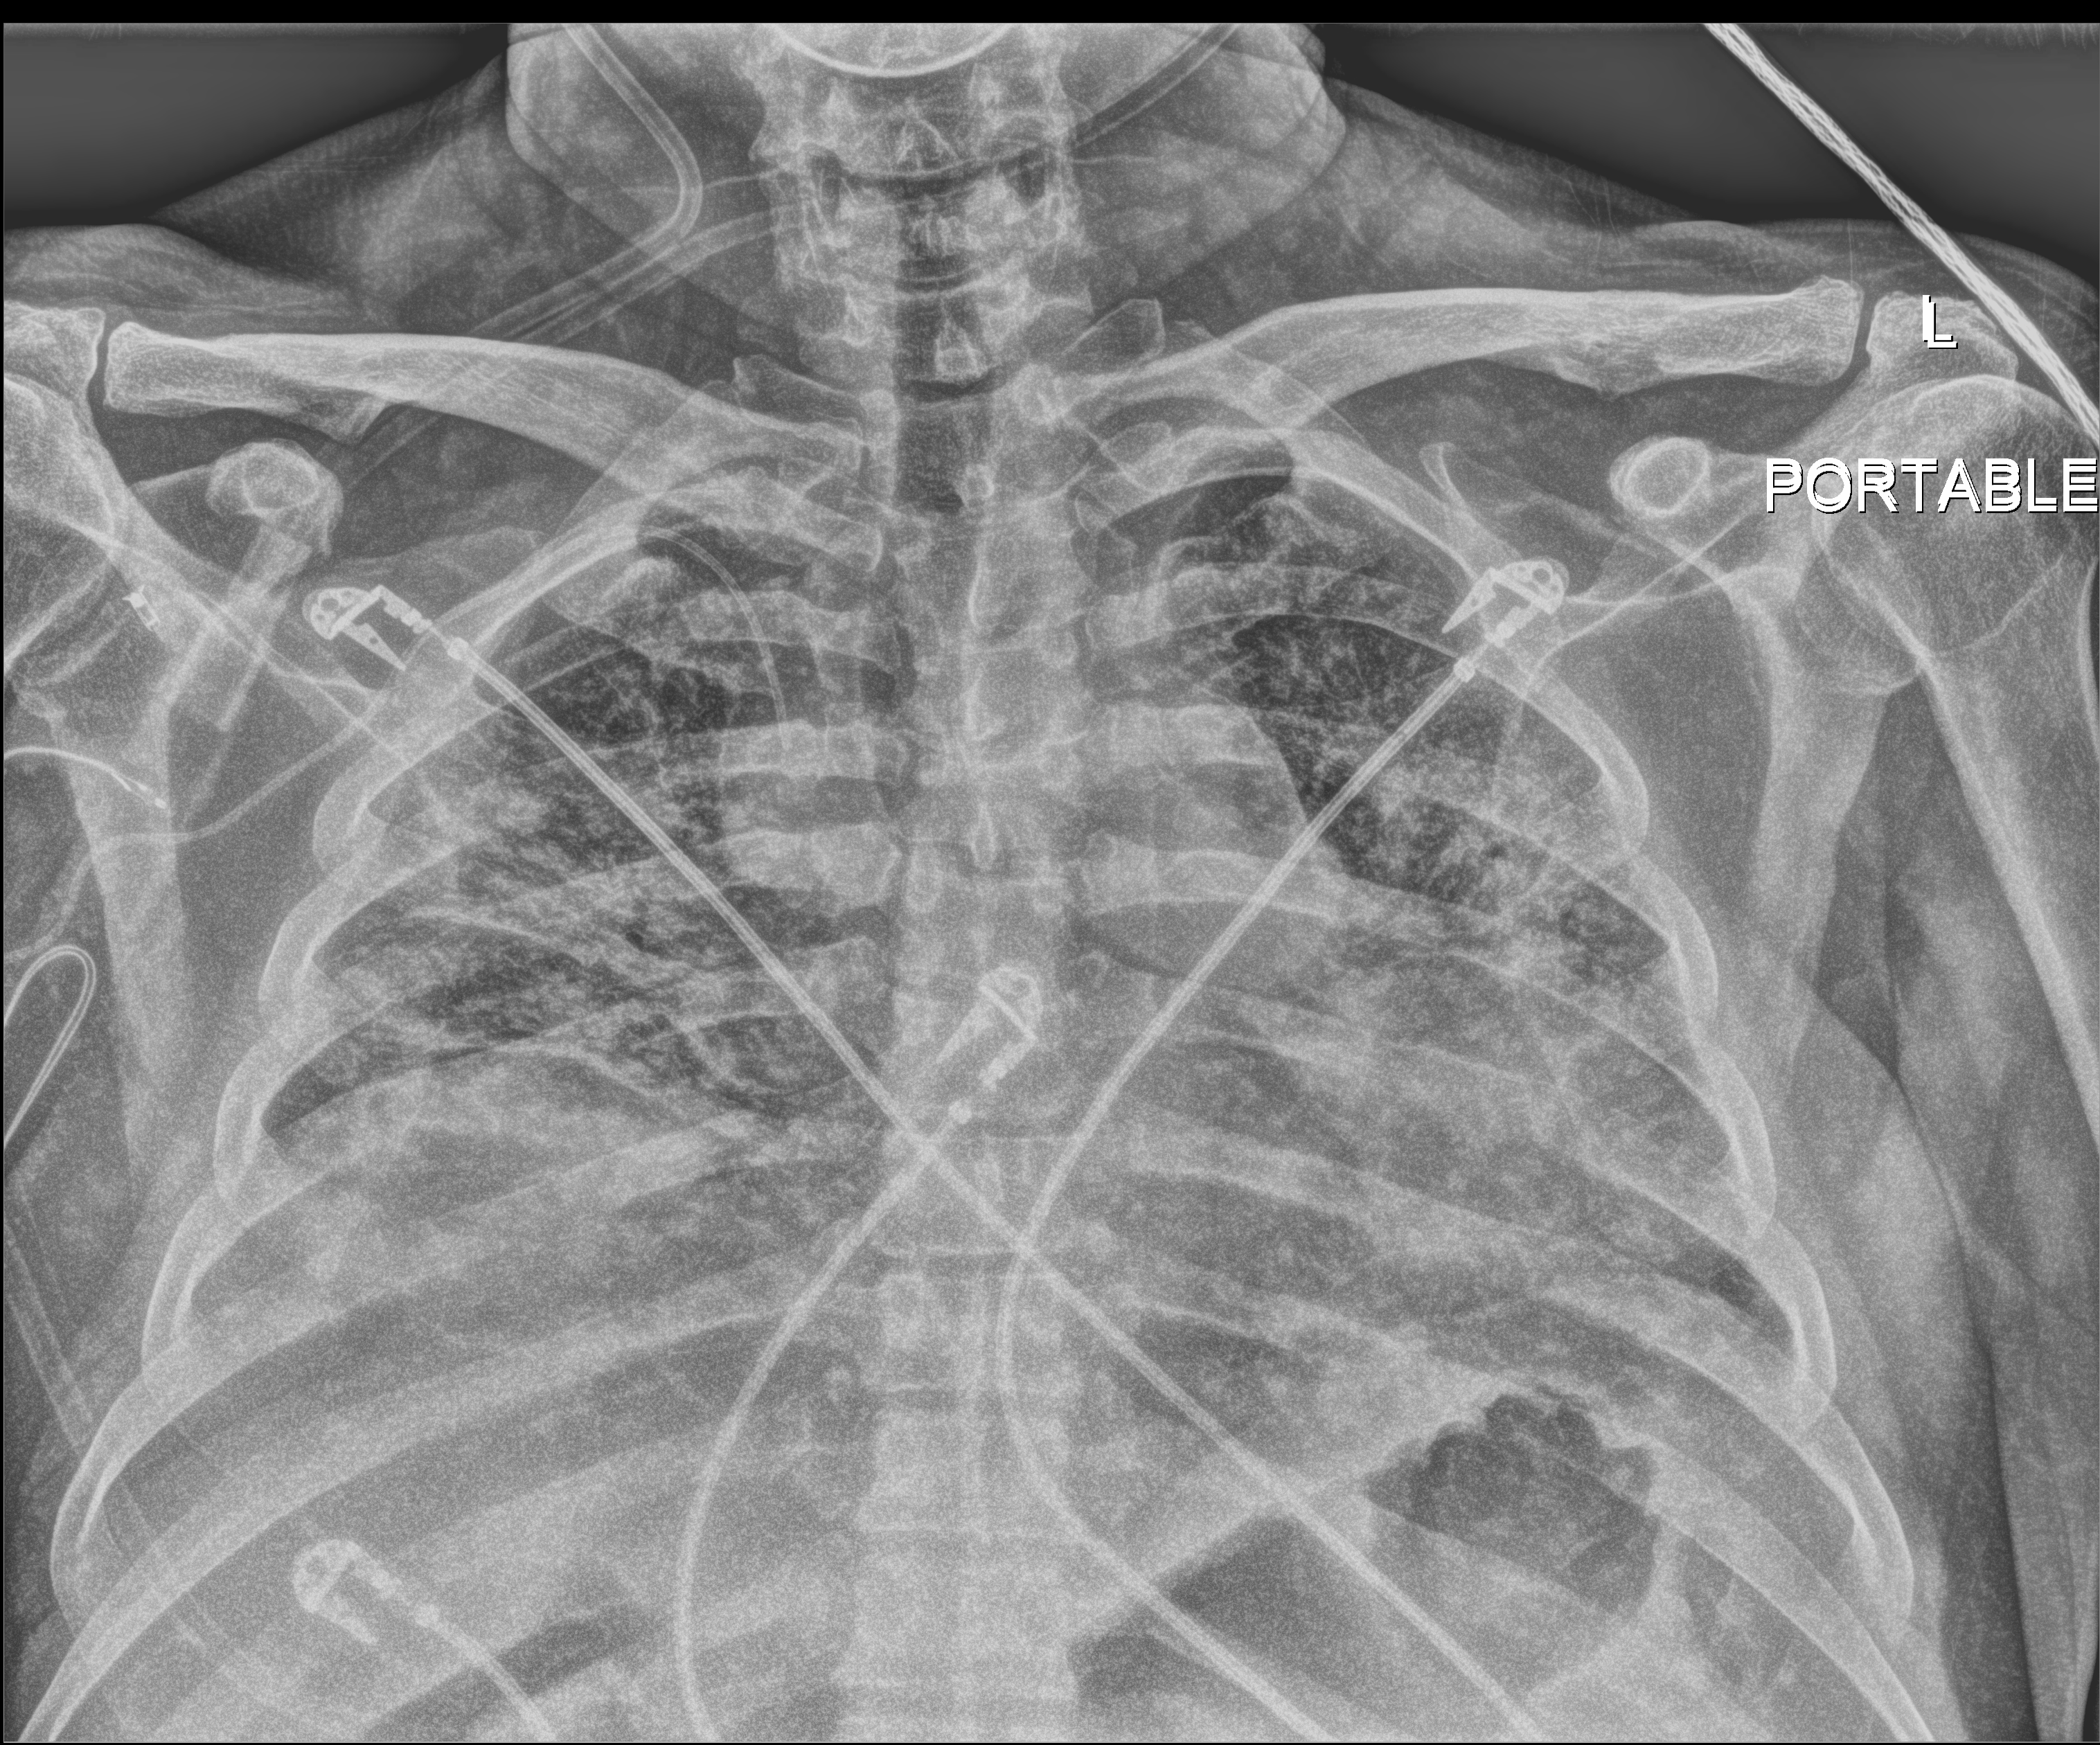
Portable chest radiograph. Male patient hospitalised with COVID-19, age 18–59 years.
From the hospital-stay record, not from the radiograph (when in the stay this image was taken is not recorded): admitted to intensive care during this hospital stay: yes.